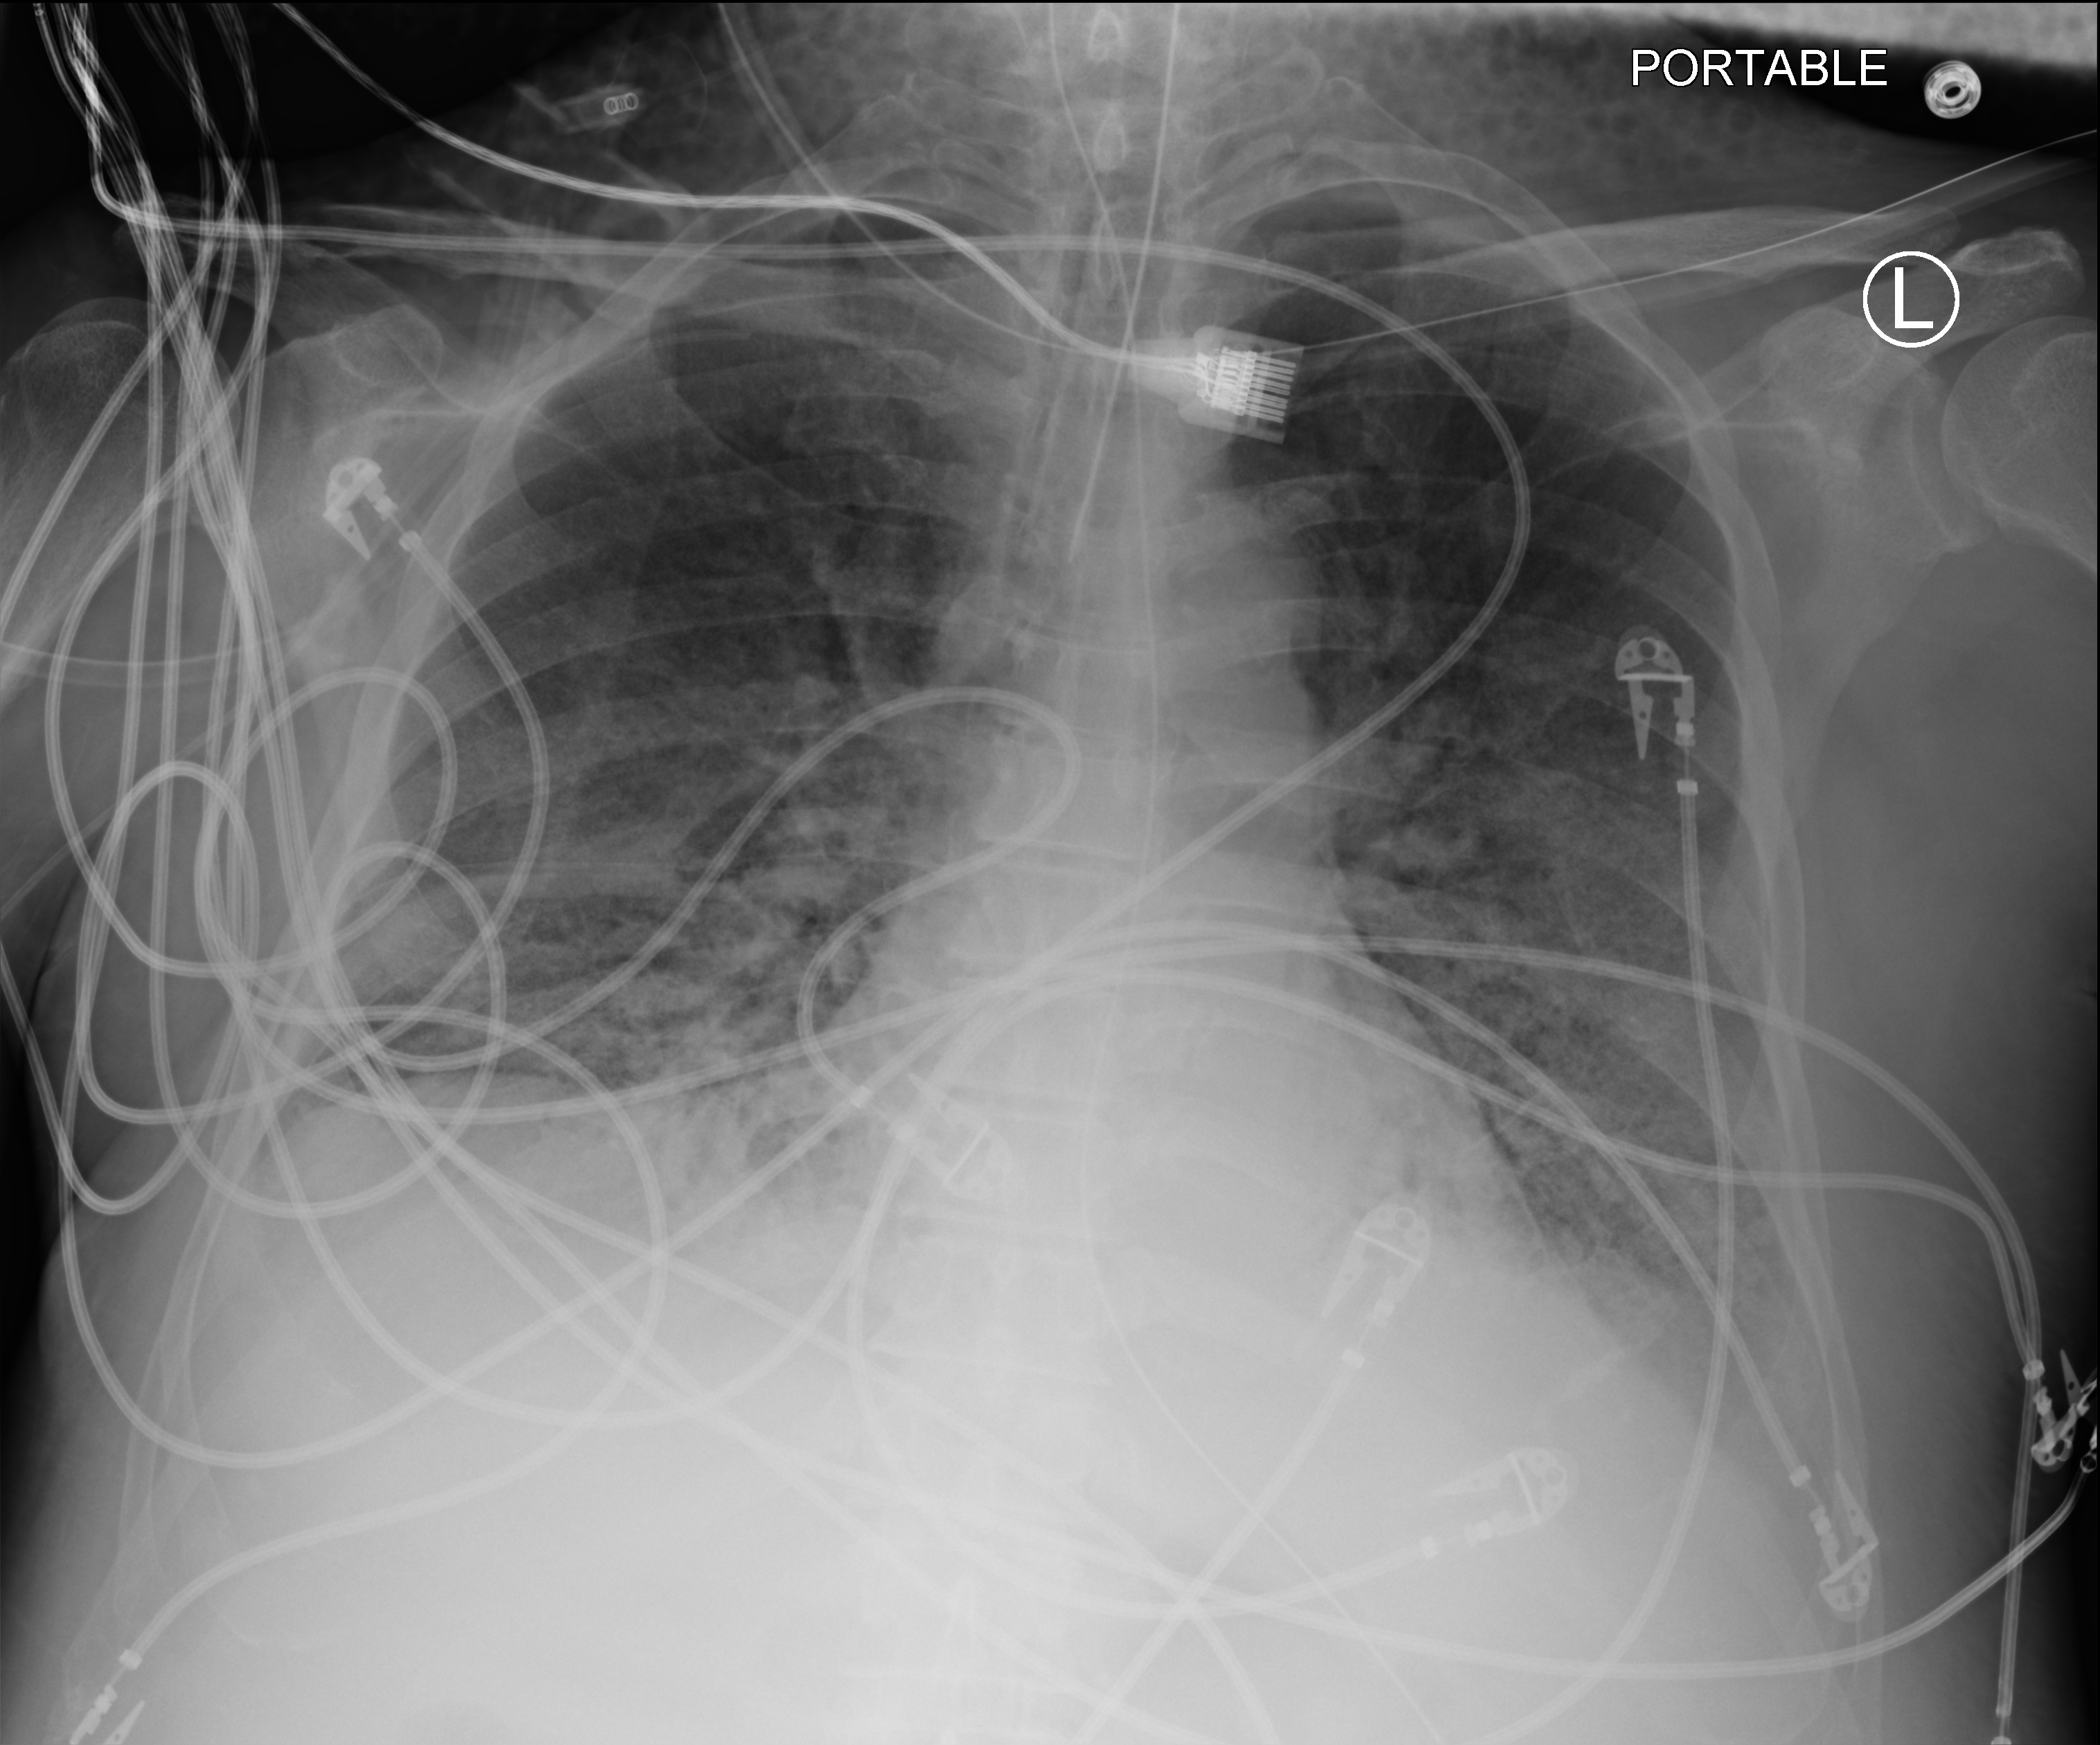
Portable chest radiograph; anteroposterior (AP) projection. Male patient hospitalised with COVID-19, age 60–74 years.
Hospital-stay facts (about this admission, not read from this image; timing relative to this image not recorded):
- mechanically ventilated during this hospital stay: yes
- hypertension (admission record): no